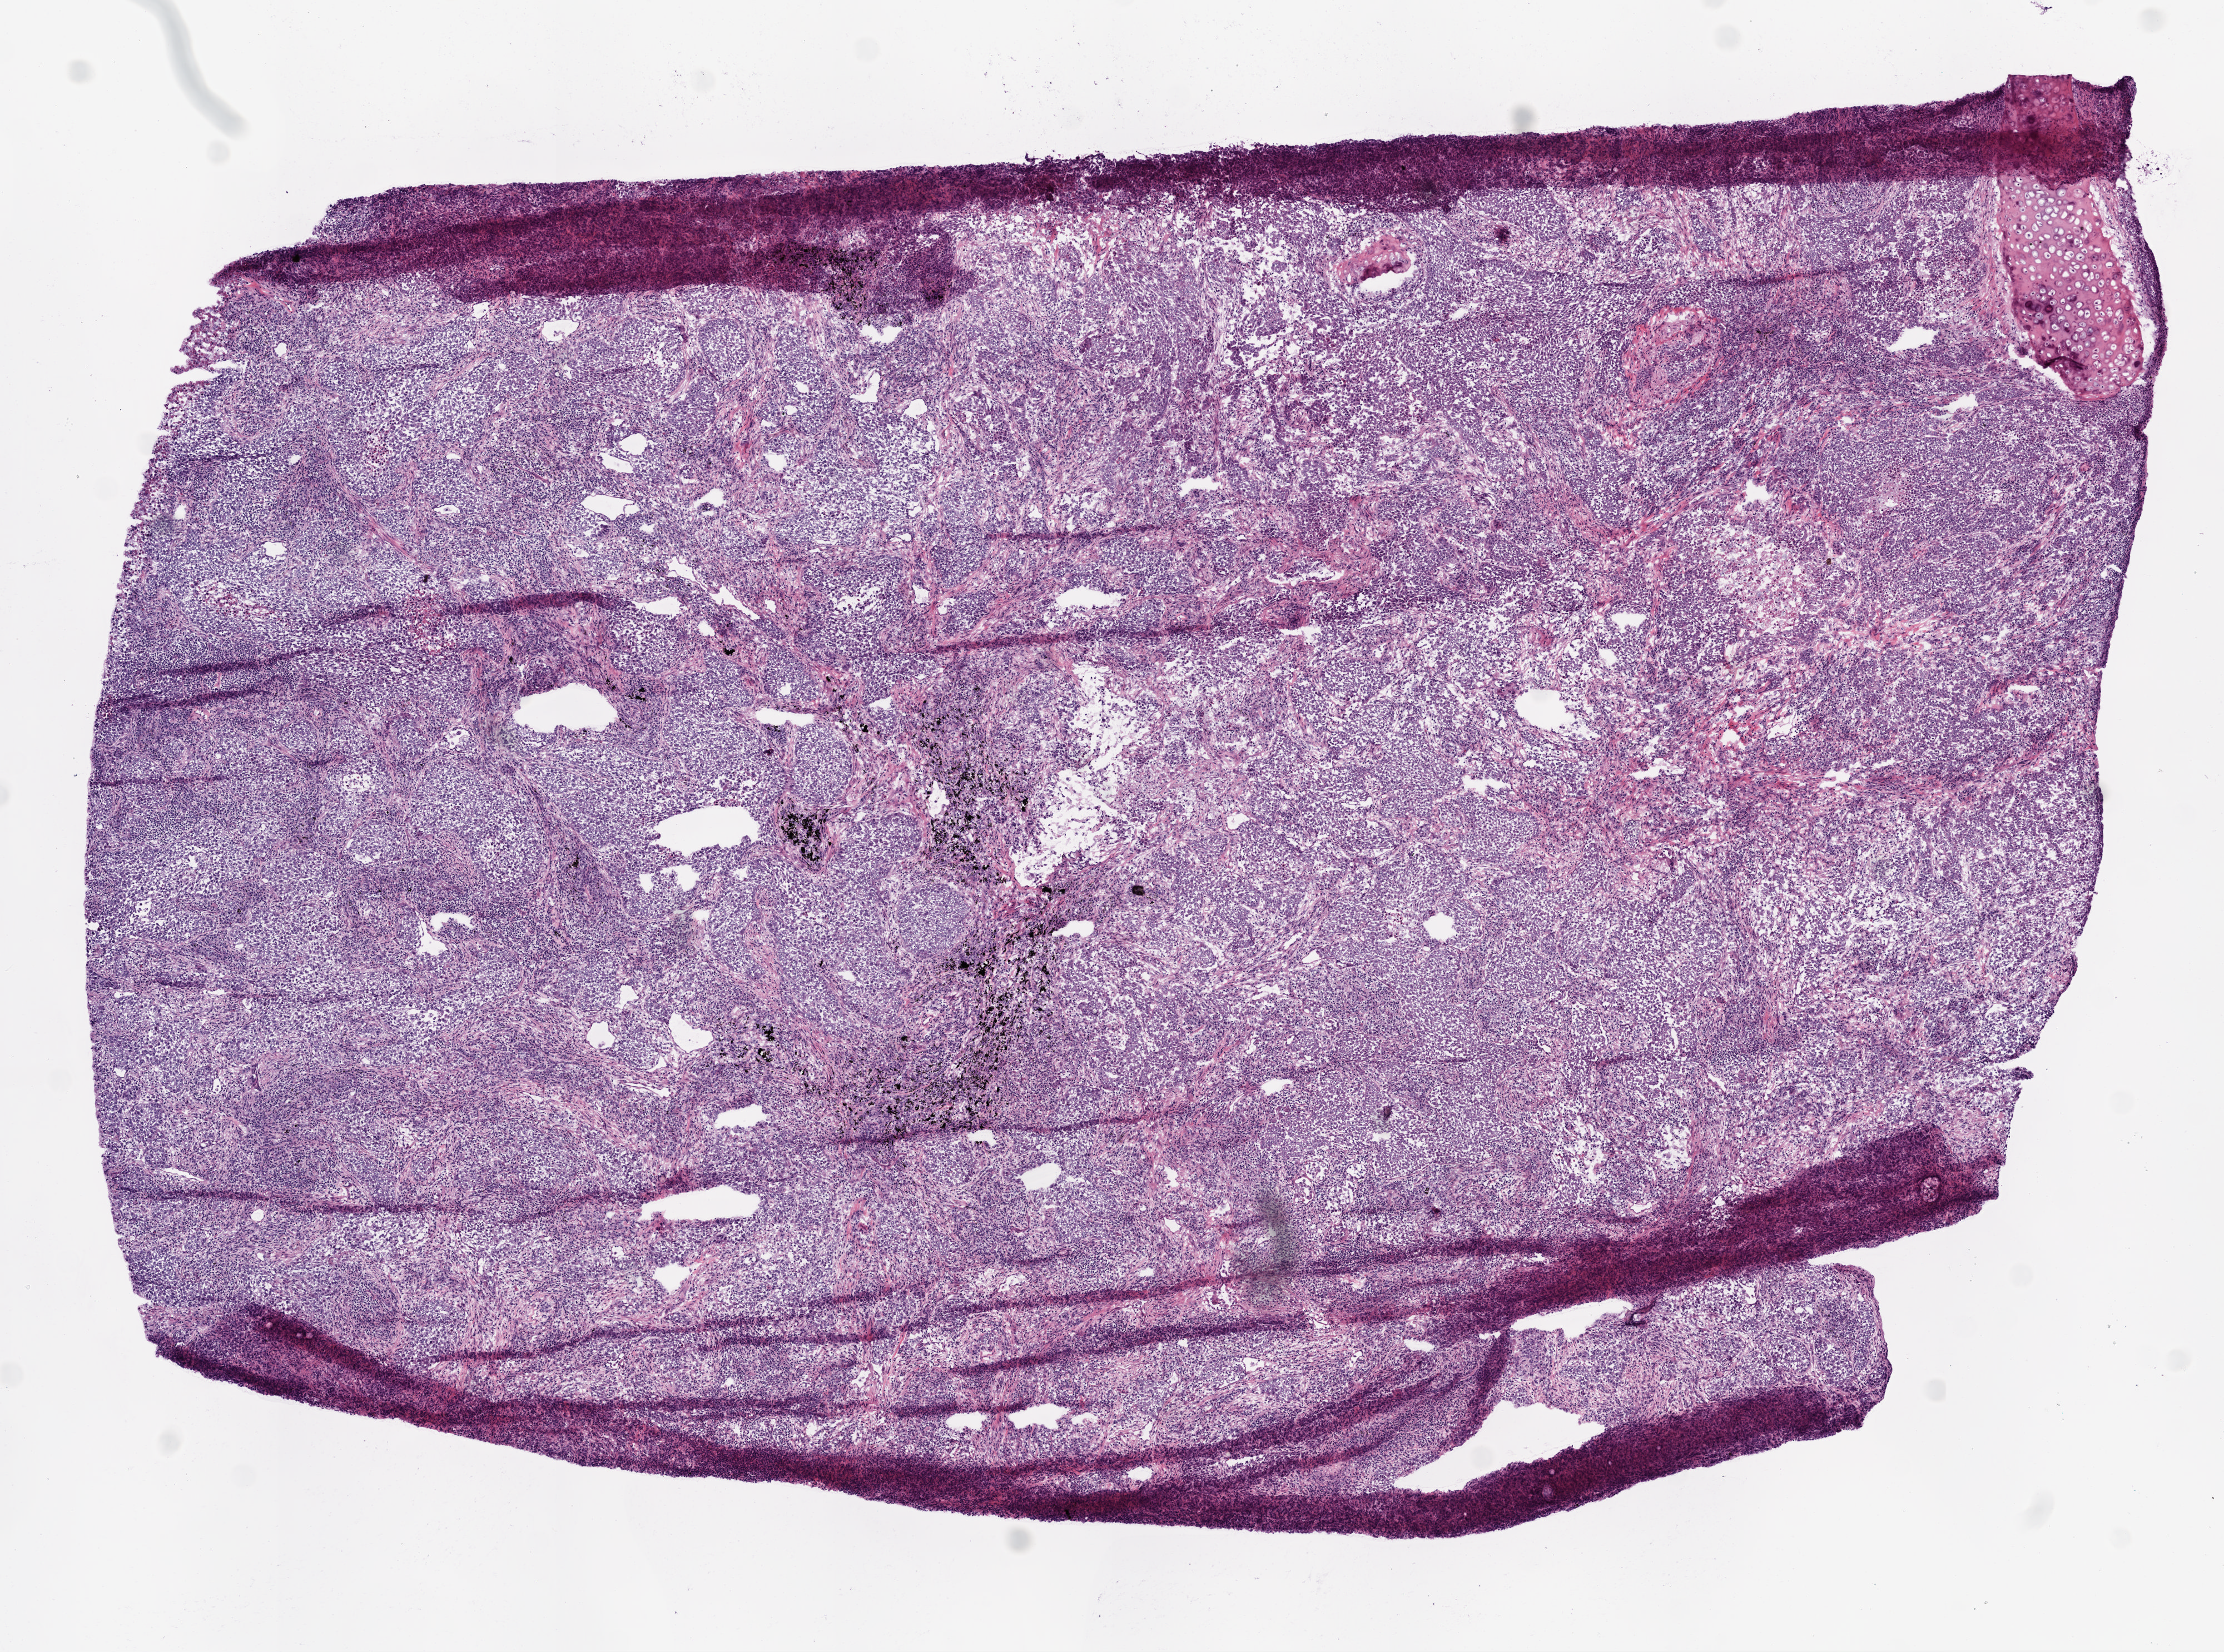
Hematoxylin and eosin (H&E) stained whole-slide image, shown as a low-resolution overview of the whole scanned area (about 8.0 x 6.0 mm). Frozen section from the top of the tissue portion. Sample: primary tumour, lung. Patient: male, age at initial diagnosis 66 years. Composition of this section per pathologist review: tumour cells 87%, tumour nuclei 70%, normal cells 5%, stromal cells 5%, necrosis 3%. Infiltration values recorded for this section: lymphocyte infiltration 20%, monocyte infiltration 1%, neutrophil infiltration 0%.
• histologic diagnosis: Squamous cell carcinoma, NOS (lower lobe, lung)
• AJCC pathologic stage: IIIB